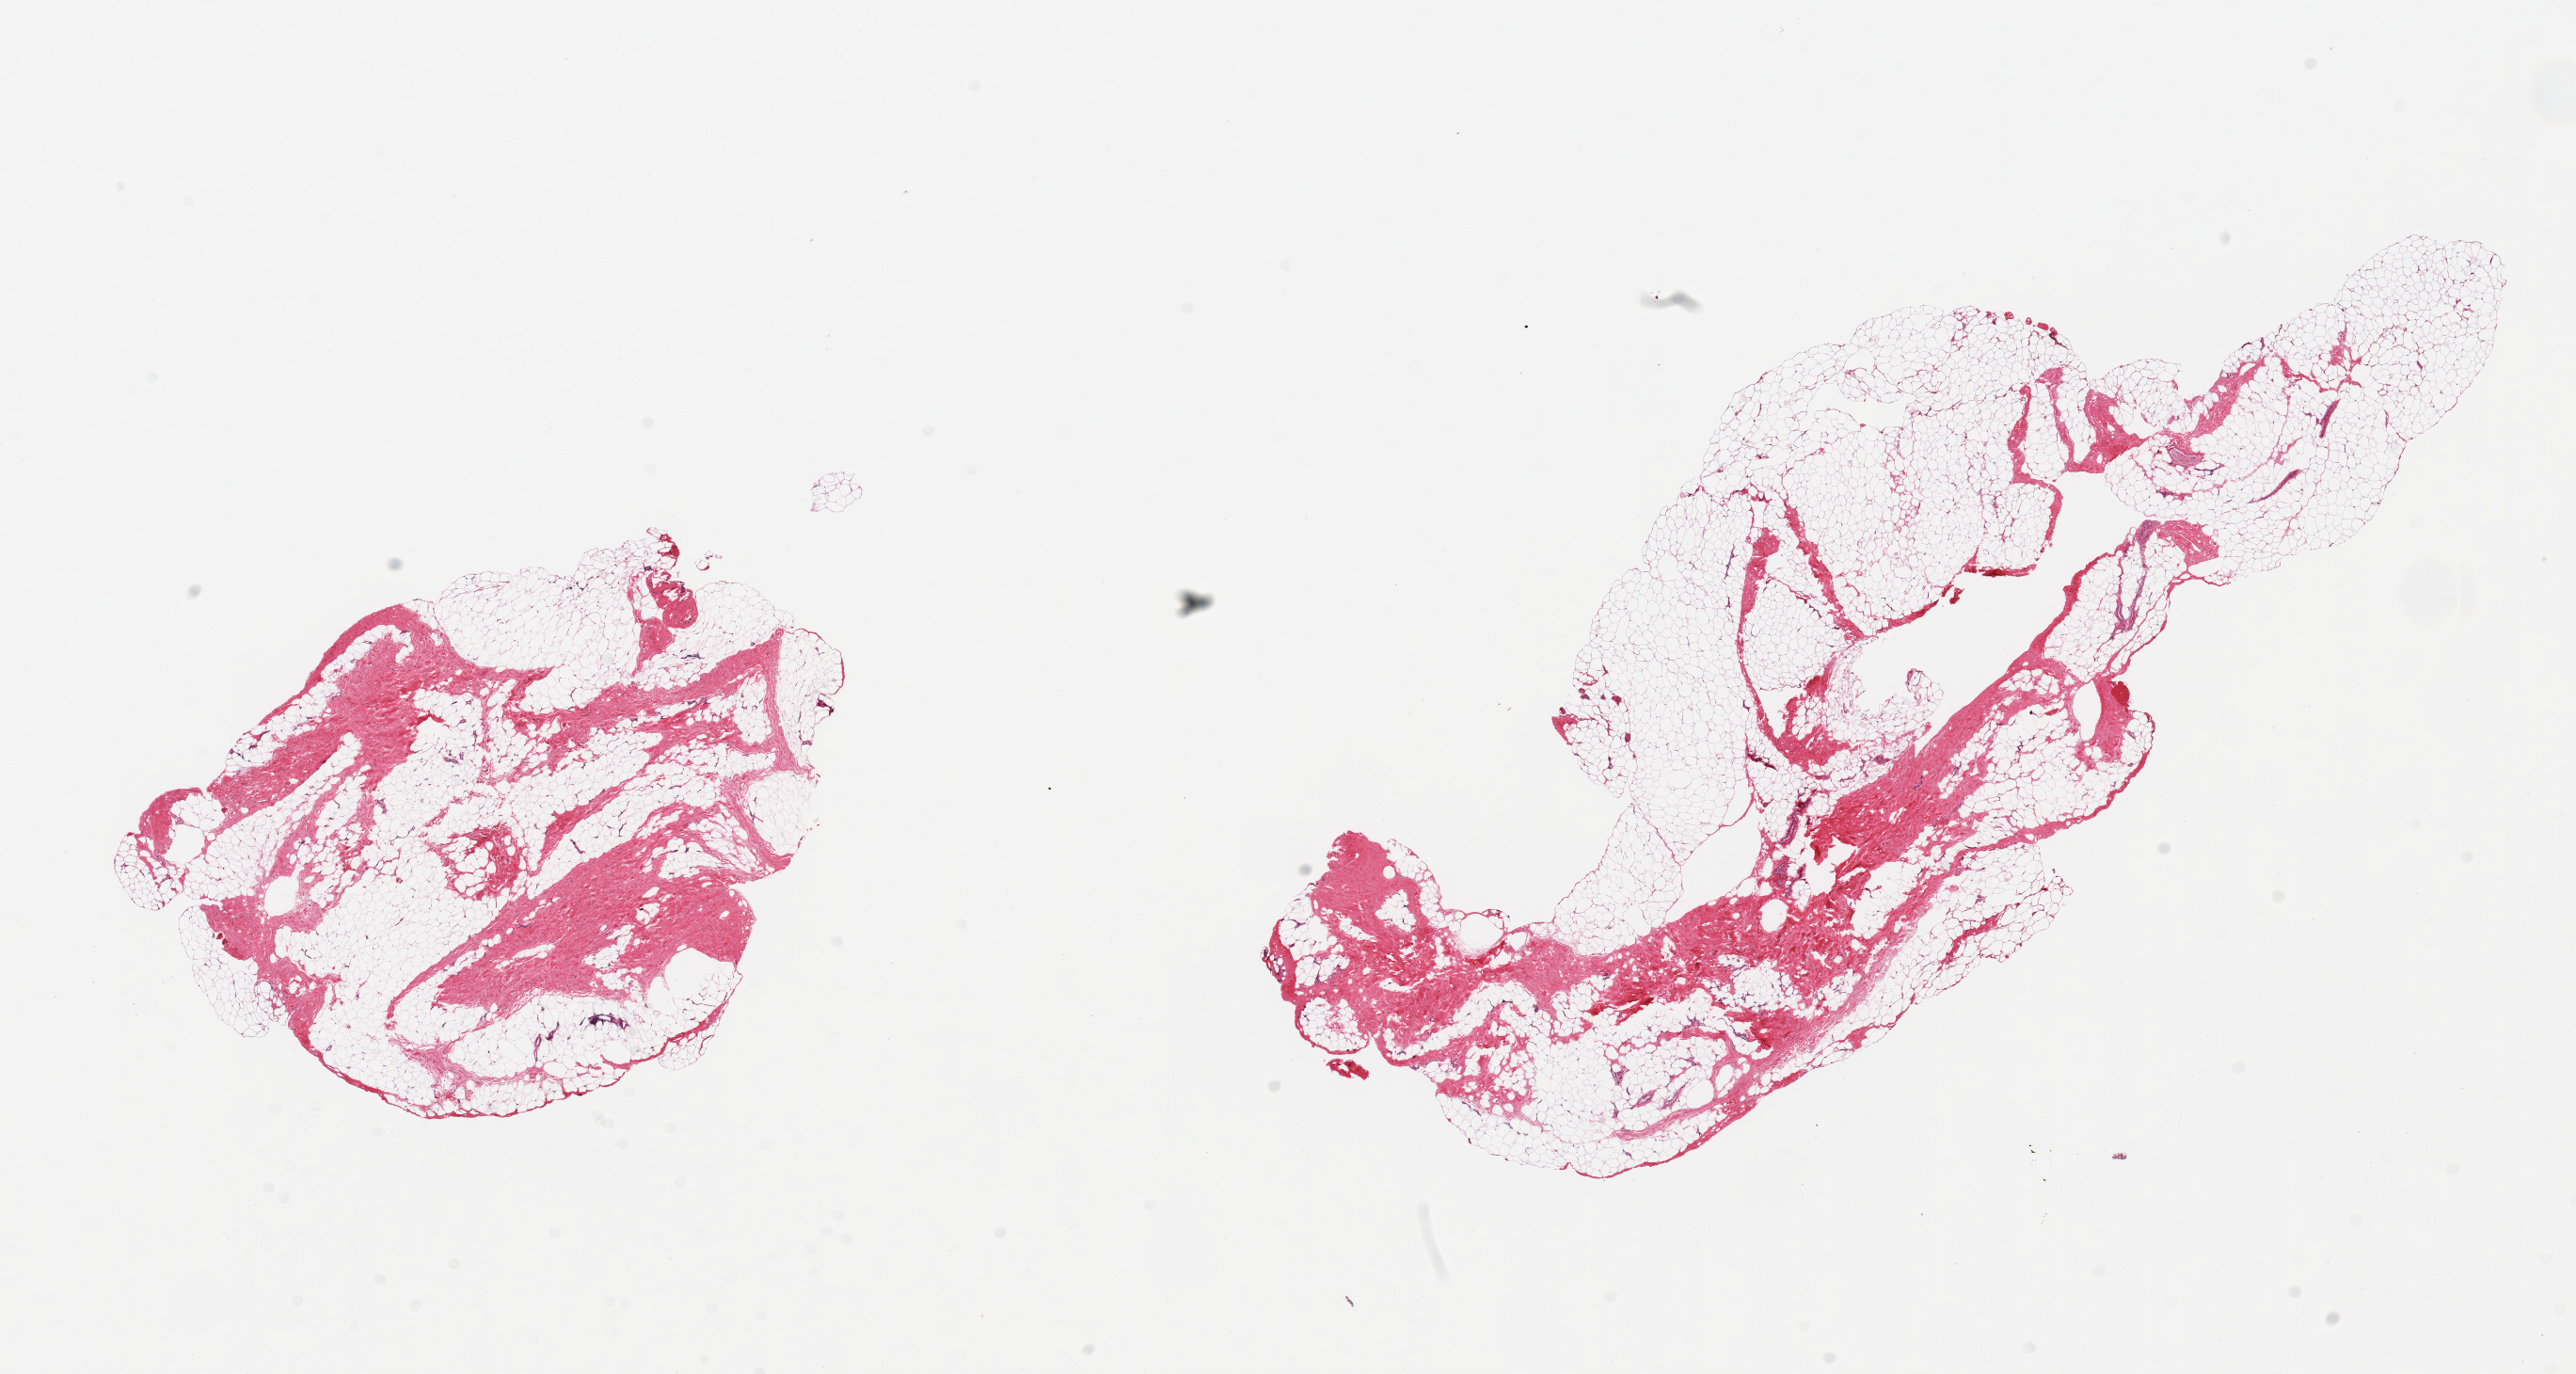
Hematoxylin and eosin (H&E) whole-slide image — whole scanned area (about 21.7 x 11.5 mm) shown as a low-resolution overview; PAXgene-fixed, paraffin-embedded tissue; sampled site (target tissue): breast; tissue donor sample. Donor sex: male.
Reviewer comment on this tissue sample: 2 pieces; fibrofatty tissue without mammary ducts.